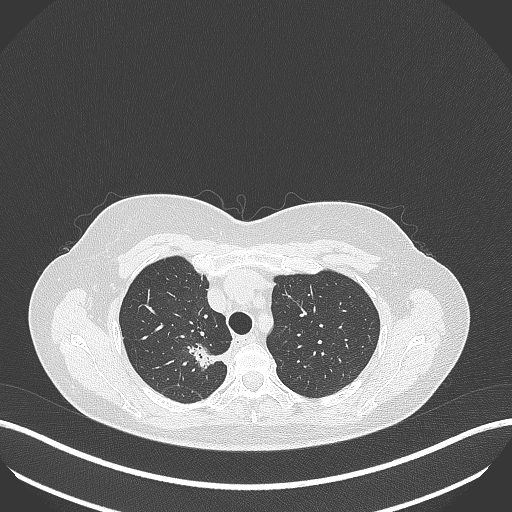
Chest CT, one axial slice. Slice 306 of 386 in the series (ordered by position). 120 kVp. Lung window (W 1500 / L -600 HU). 1 mm slice thickness. 512 × 512 image matrix, field of view 400 × 400 mm. Patient: female, 65 years. From the clinical record (not read from this slice): clinical TNM (as recorded): T1b N0 M0.
Outlined on this slice (bounding box drawn by a radiologist):
- lung tumour (recorded histology: adenocarcinoma): bounding box <187,342,231,374> (left, top, right, bottom; pixels)